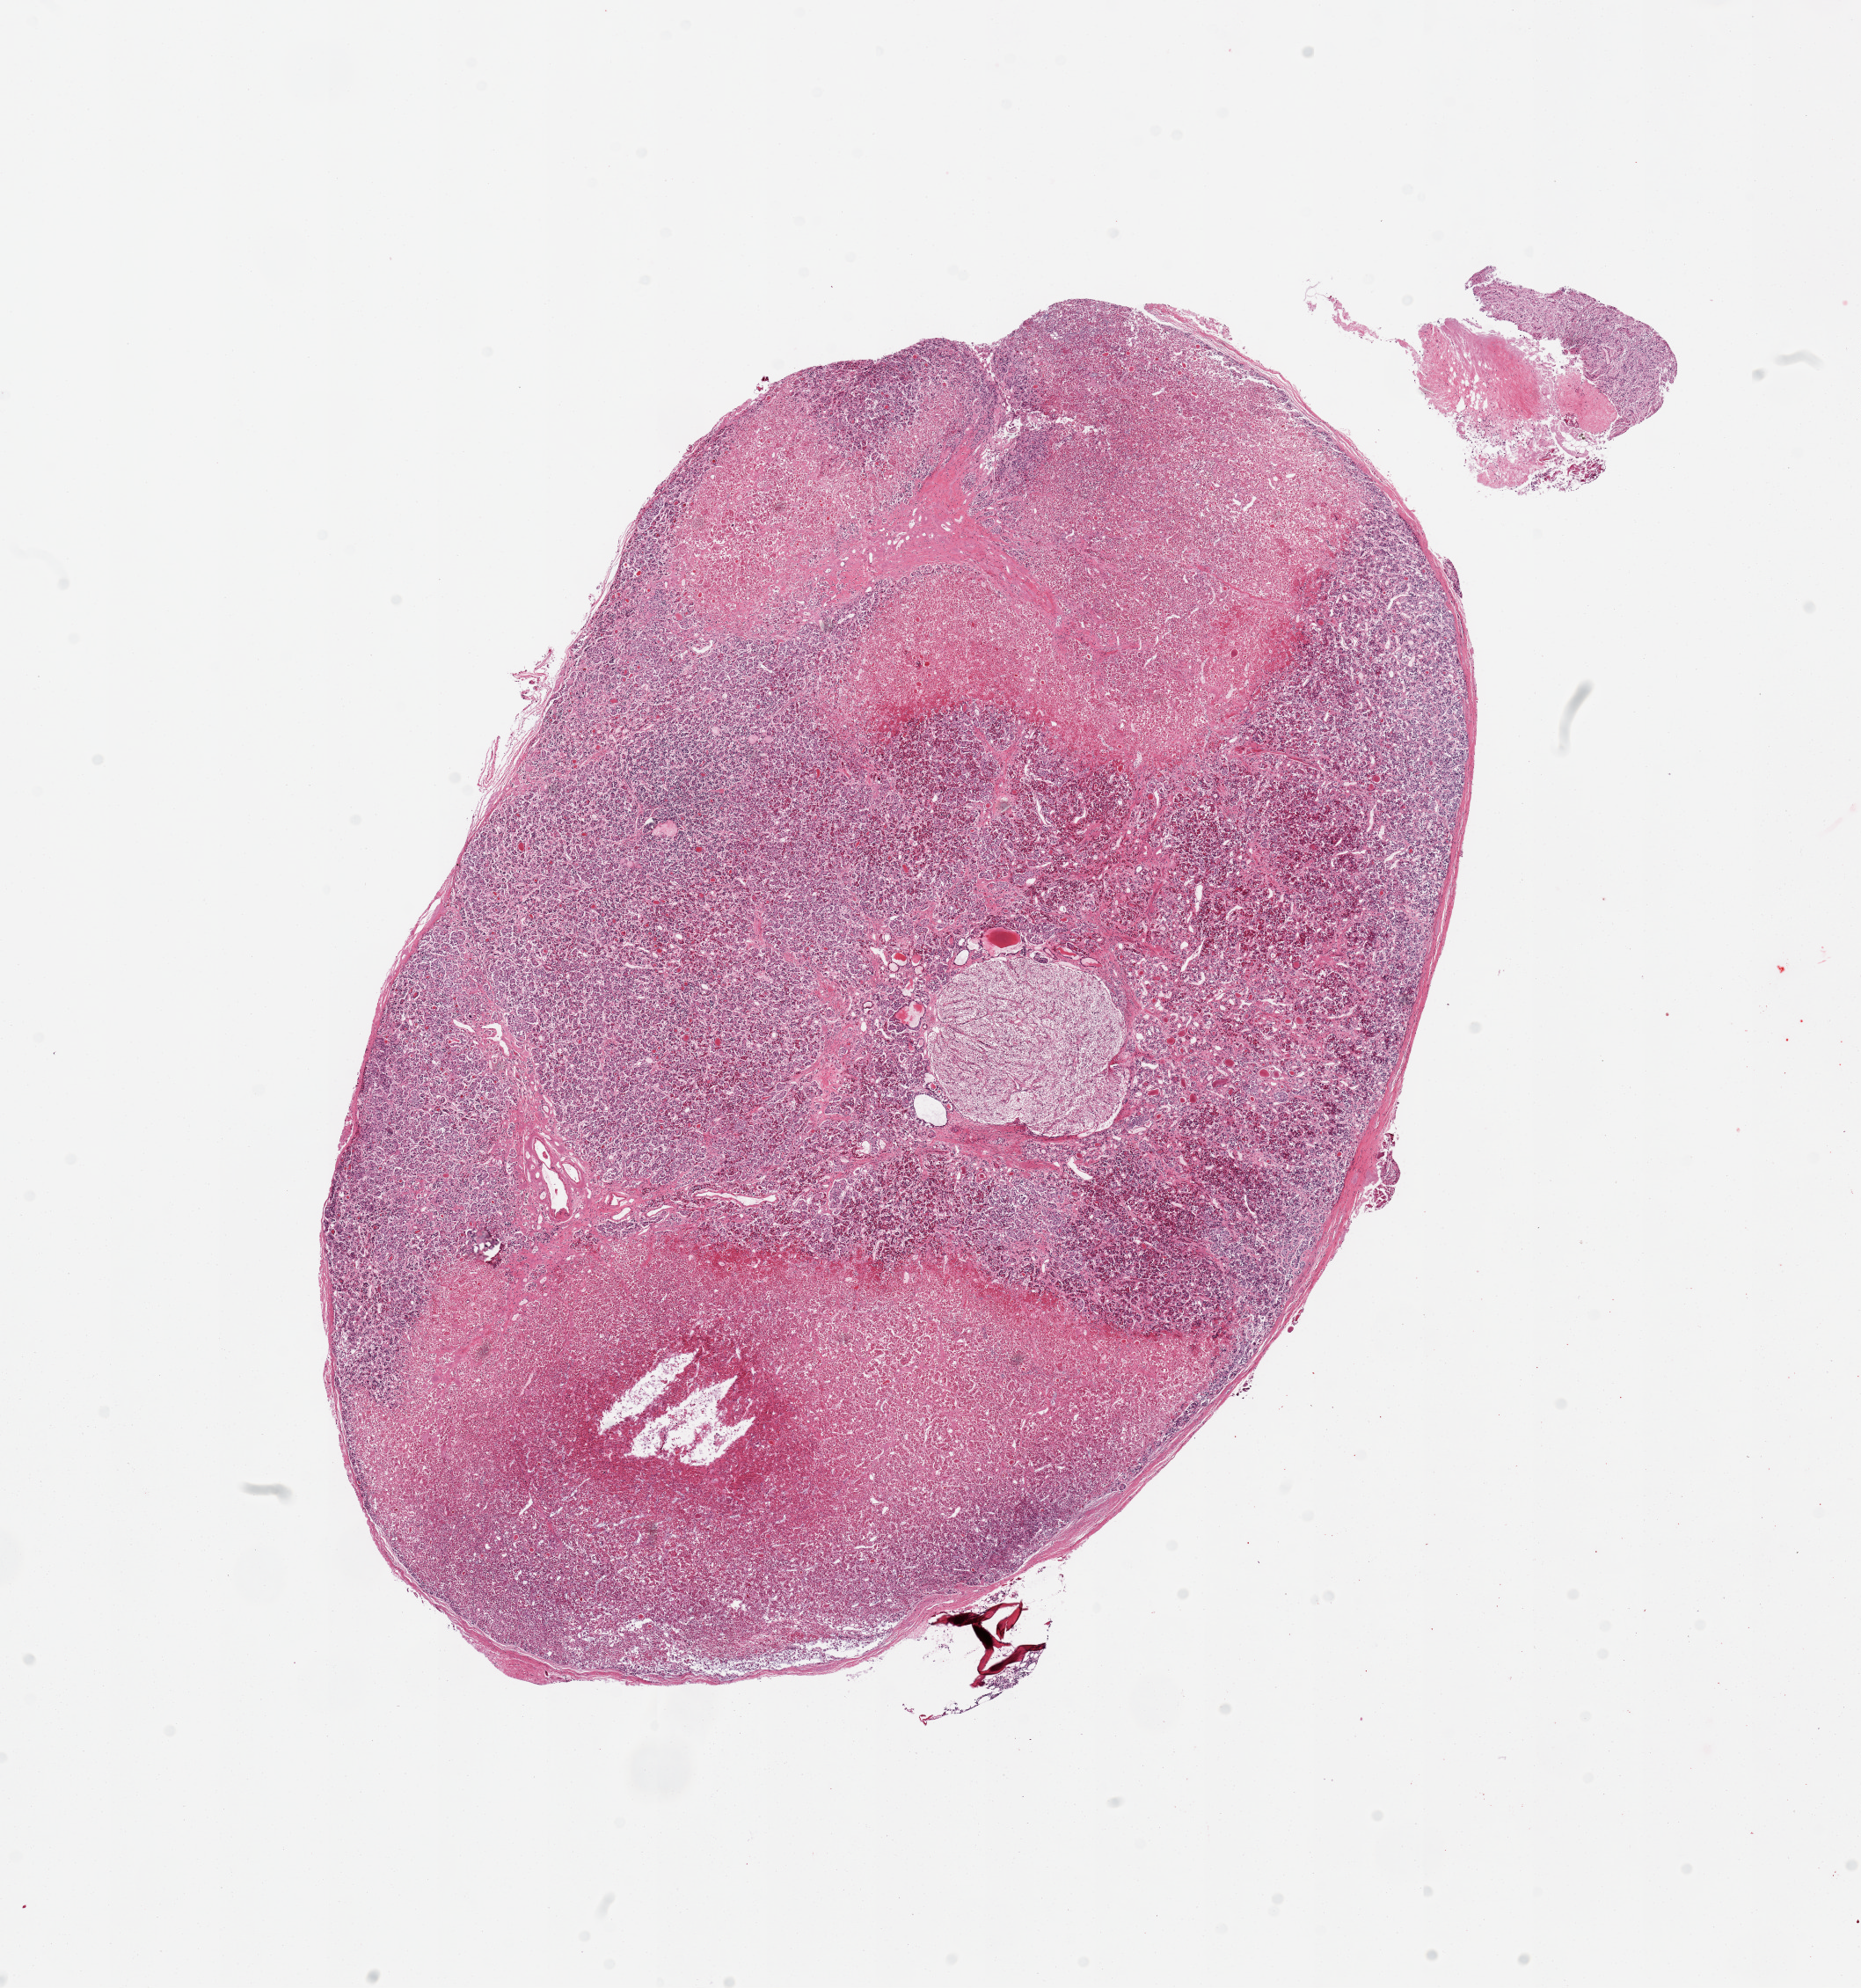
Whole-slide image, H&E stain, brightfield — shown as a low-resolution overview of the whole scanned area (about 16.7 x 17.9 mm, slide scanned at 20x). PAXgene-fixed paraffin-embedded (PFPE) section. Sampled site (target tissue): pituitary. Tissue donor sample. Male donor.
Review note (as recorded): 1 pieces, adenohypophysis, focally infarcted.